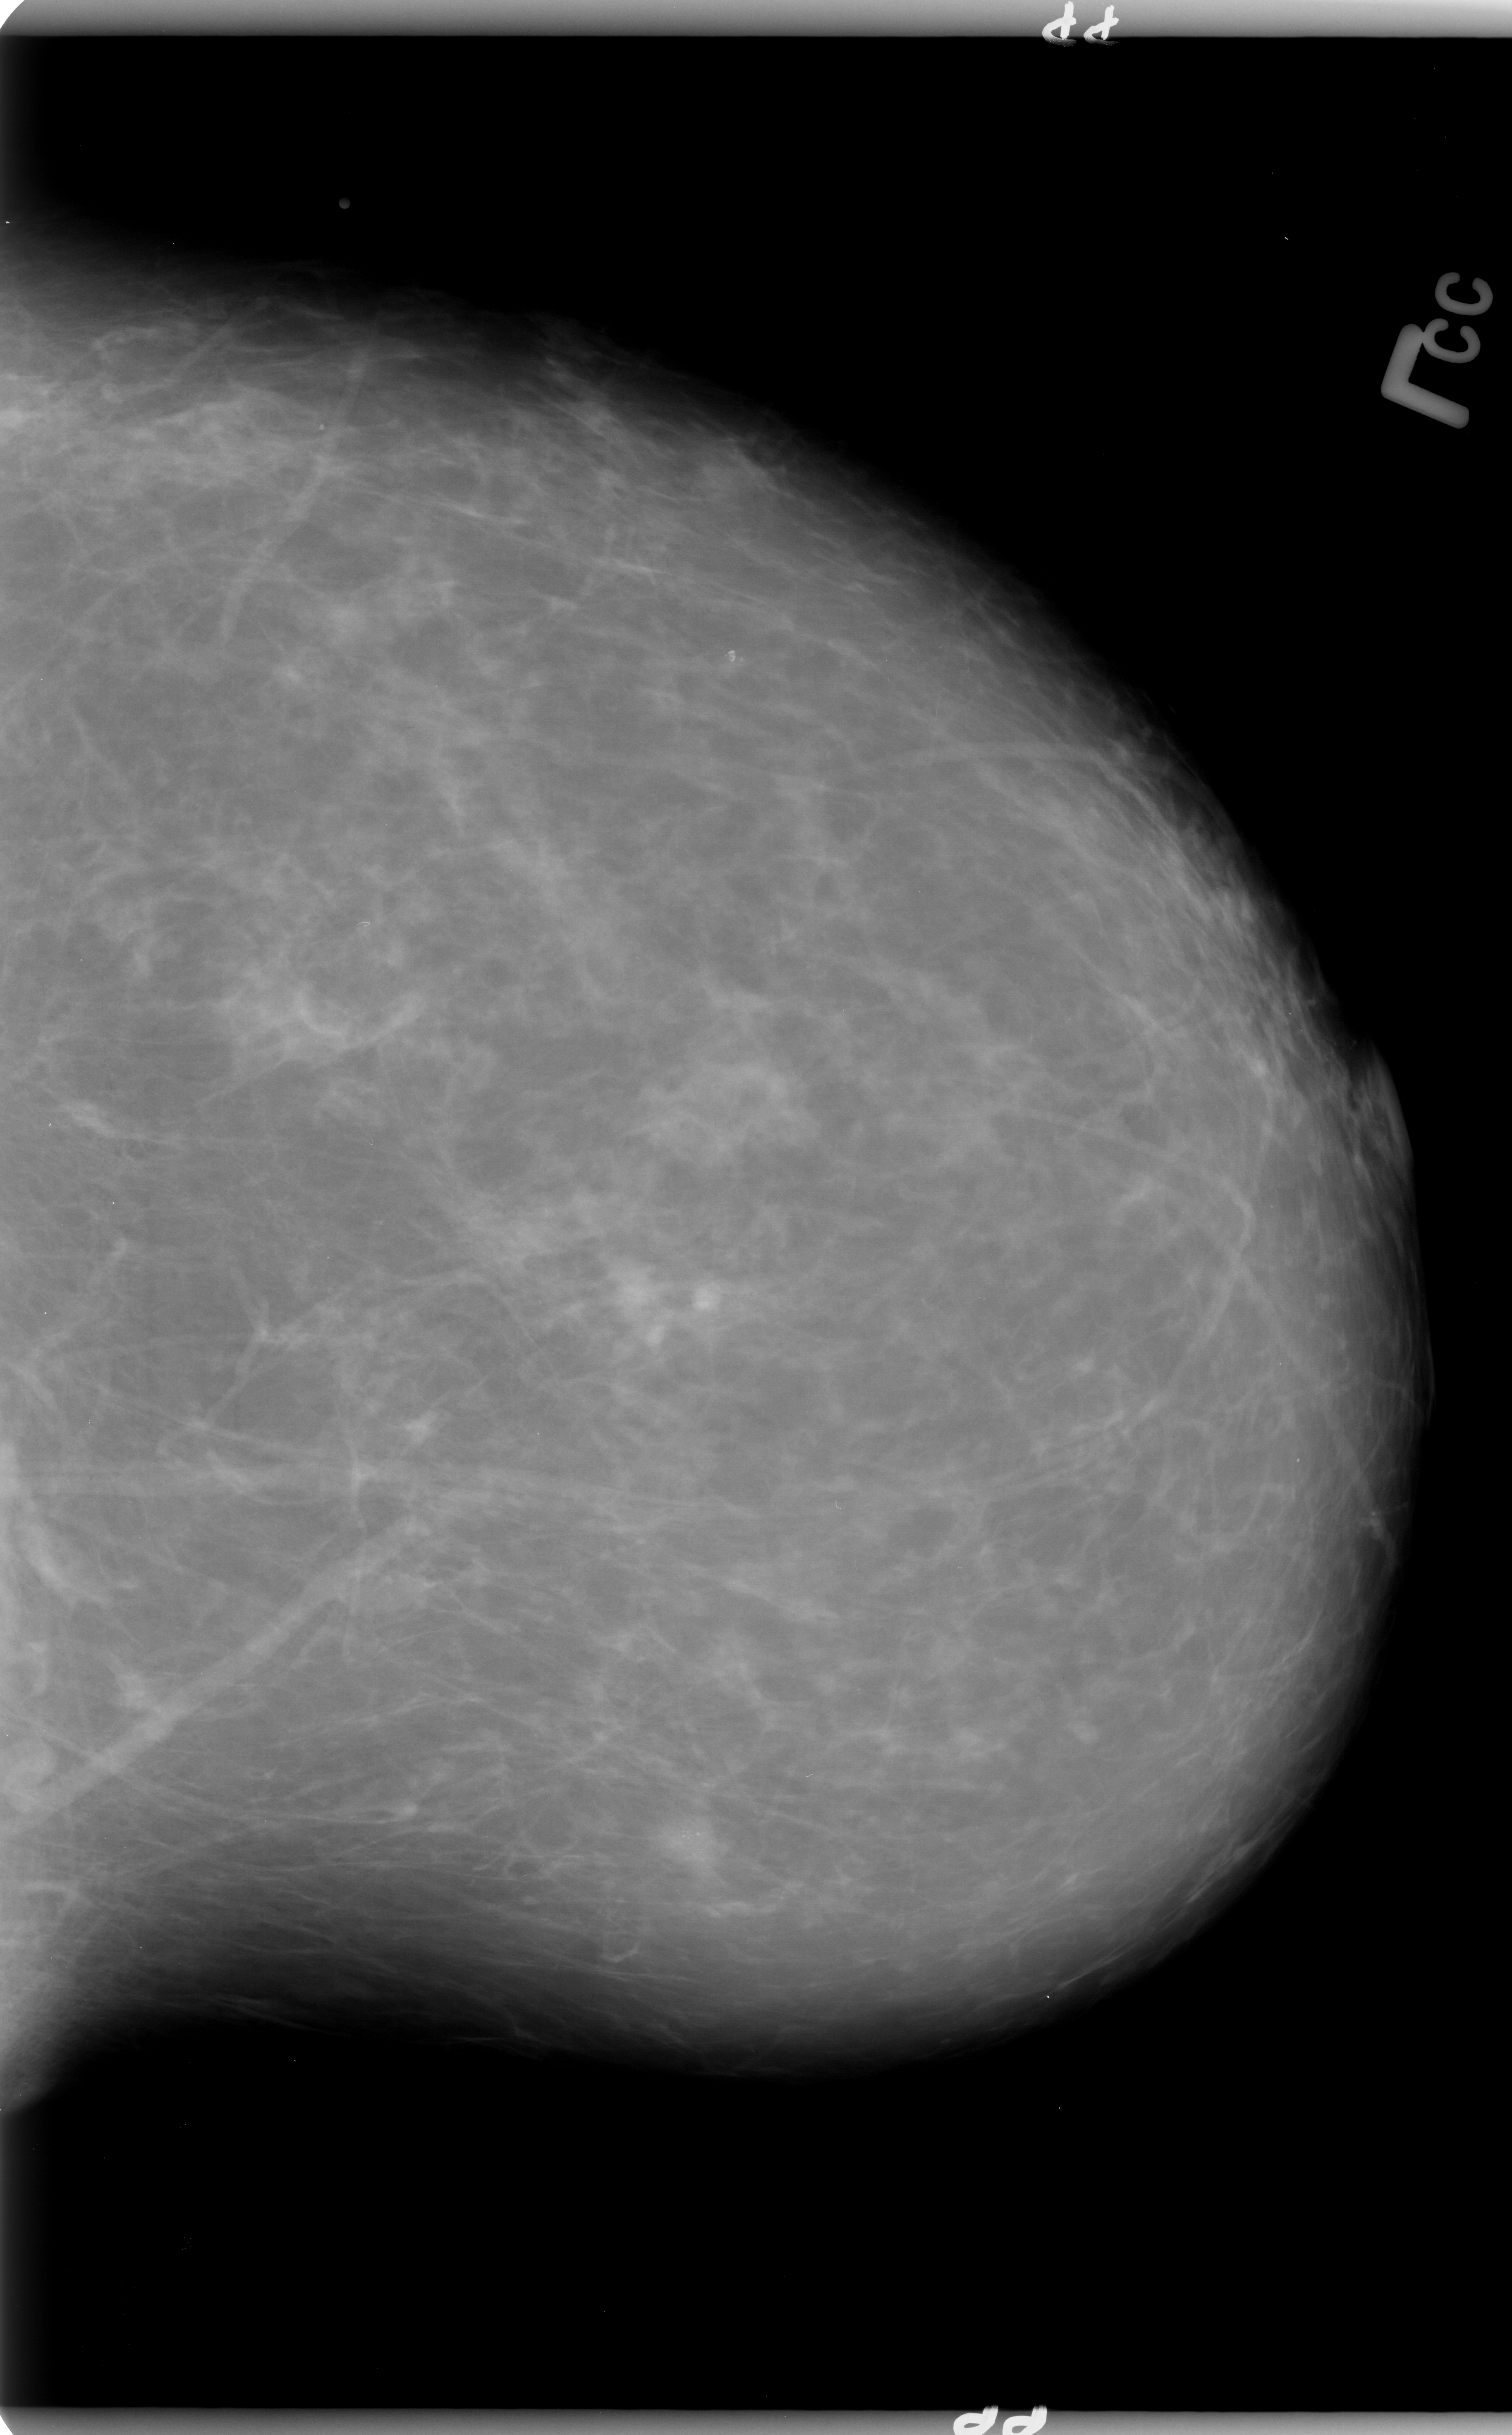
Digitized screen-film mammogram. Left breast. Craniocaudal (CC) view. BI-RADS breast density category 2 (scale 1–4). 1512 × 2435 image matrix.
Expert-marked regions of interest on this image (one box per marked abnormality):
- calcifications, morphology pleomorphic, distribution clustered; BI-RADS assessment category 4; subtlety rating 3 on a 1 (subtle) to 5 (obvious) scale; pathology result (as recorded, not read from the image): benign: box from (x=635, y=1816) to (x=785, y=1923) px